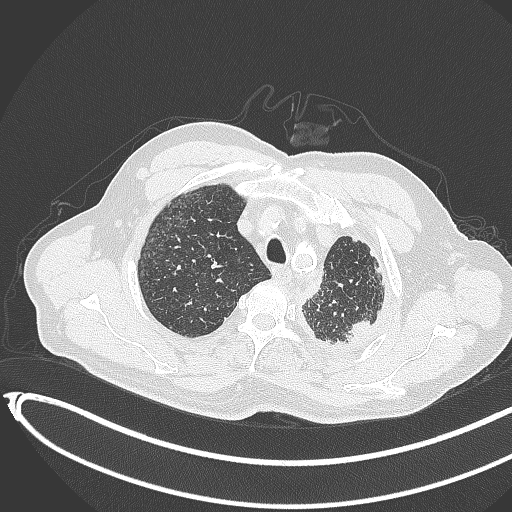
Chest CT, one axial slice. Position 361 of 451 along the scan axis. 120 kVp. Lung window (W 1500 / L -600 HU). 512 × 512 image matrix, field of view 400 × 400 mm. Male patient, age 78 years. From the clinical record (not read from this slice): clinical TNM (as recorded): T1c N0 M1.
Structures marked on this image (bounding box drawn by a radiologist):
- lung tumour (recorded histology: adenocarcinoma): bounding box [x1, y1, x2, y2] px = [336, 315, 376, 353]